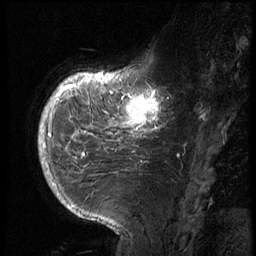
Breast MRI (dynamic contrast-enhanced), one sagittal slice; position 19 of 72 along the scan axis; 3 images stored at this slice position (order not interpretable as contrast timing); 1.5 T; TE 4.2 ms, TR 8.9 ms; 2.5 mm slice thickness; 256 × 256 image matrix, field of view 200 × 200 mm. Female patient, age 56 years. From the clinical record (not read from this slice): setting: breast cancer imaged before/during neoadjuvant chemotherapy.
Annotated regions visible in this slice (semi-automatic segmentation, software-assisted and operator-edited):
- analysis volume of interest (the breast-tissue region the enhancement analysis was run in; not a lesion): bounding box [x1, y1, x2, y2] px = [114, 76, 177, 138]
- tumour enhancement mask (voxels above the 140 % enhancement threshold inside the analysis volume of interest): [125, 89, 163, 132]